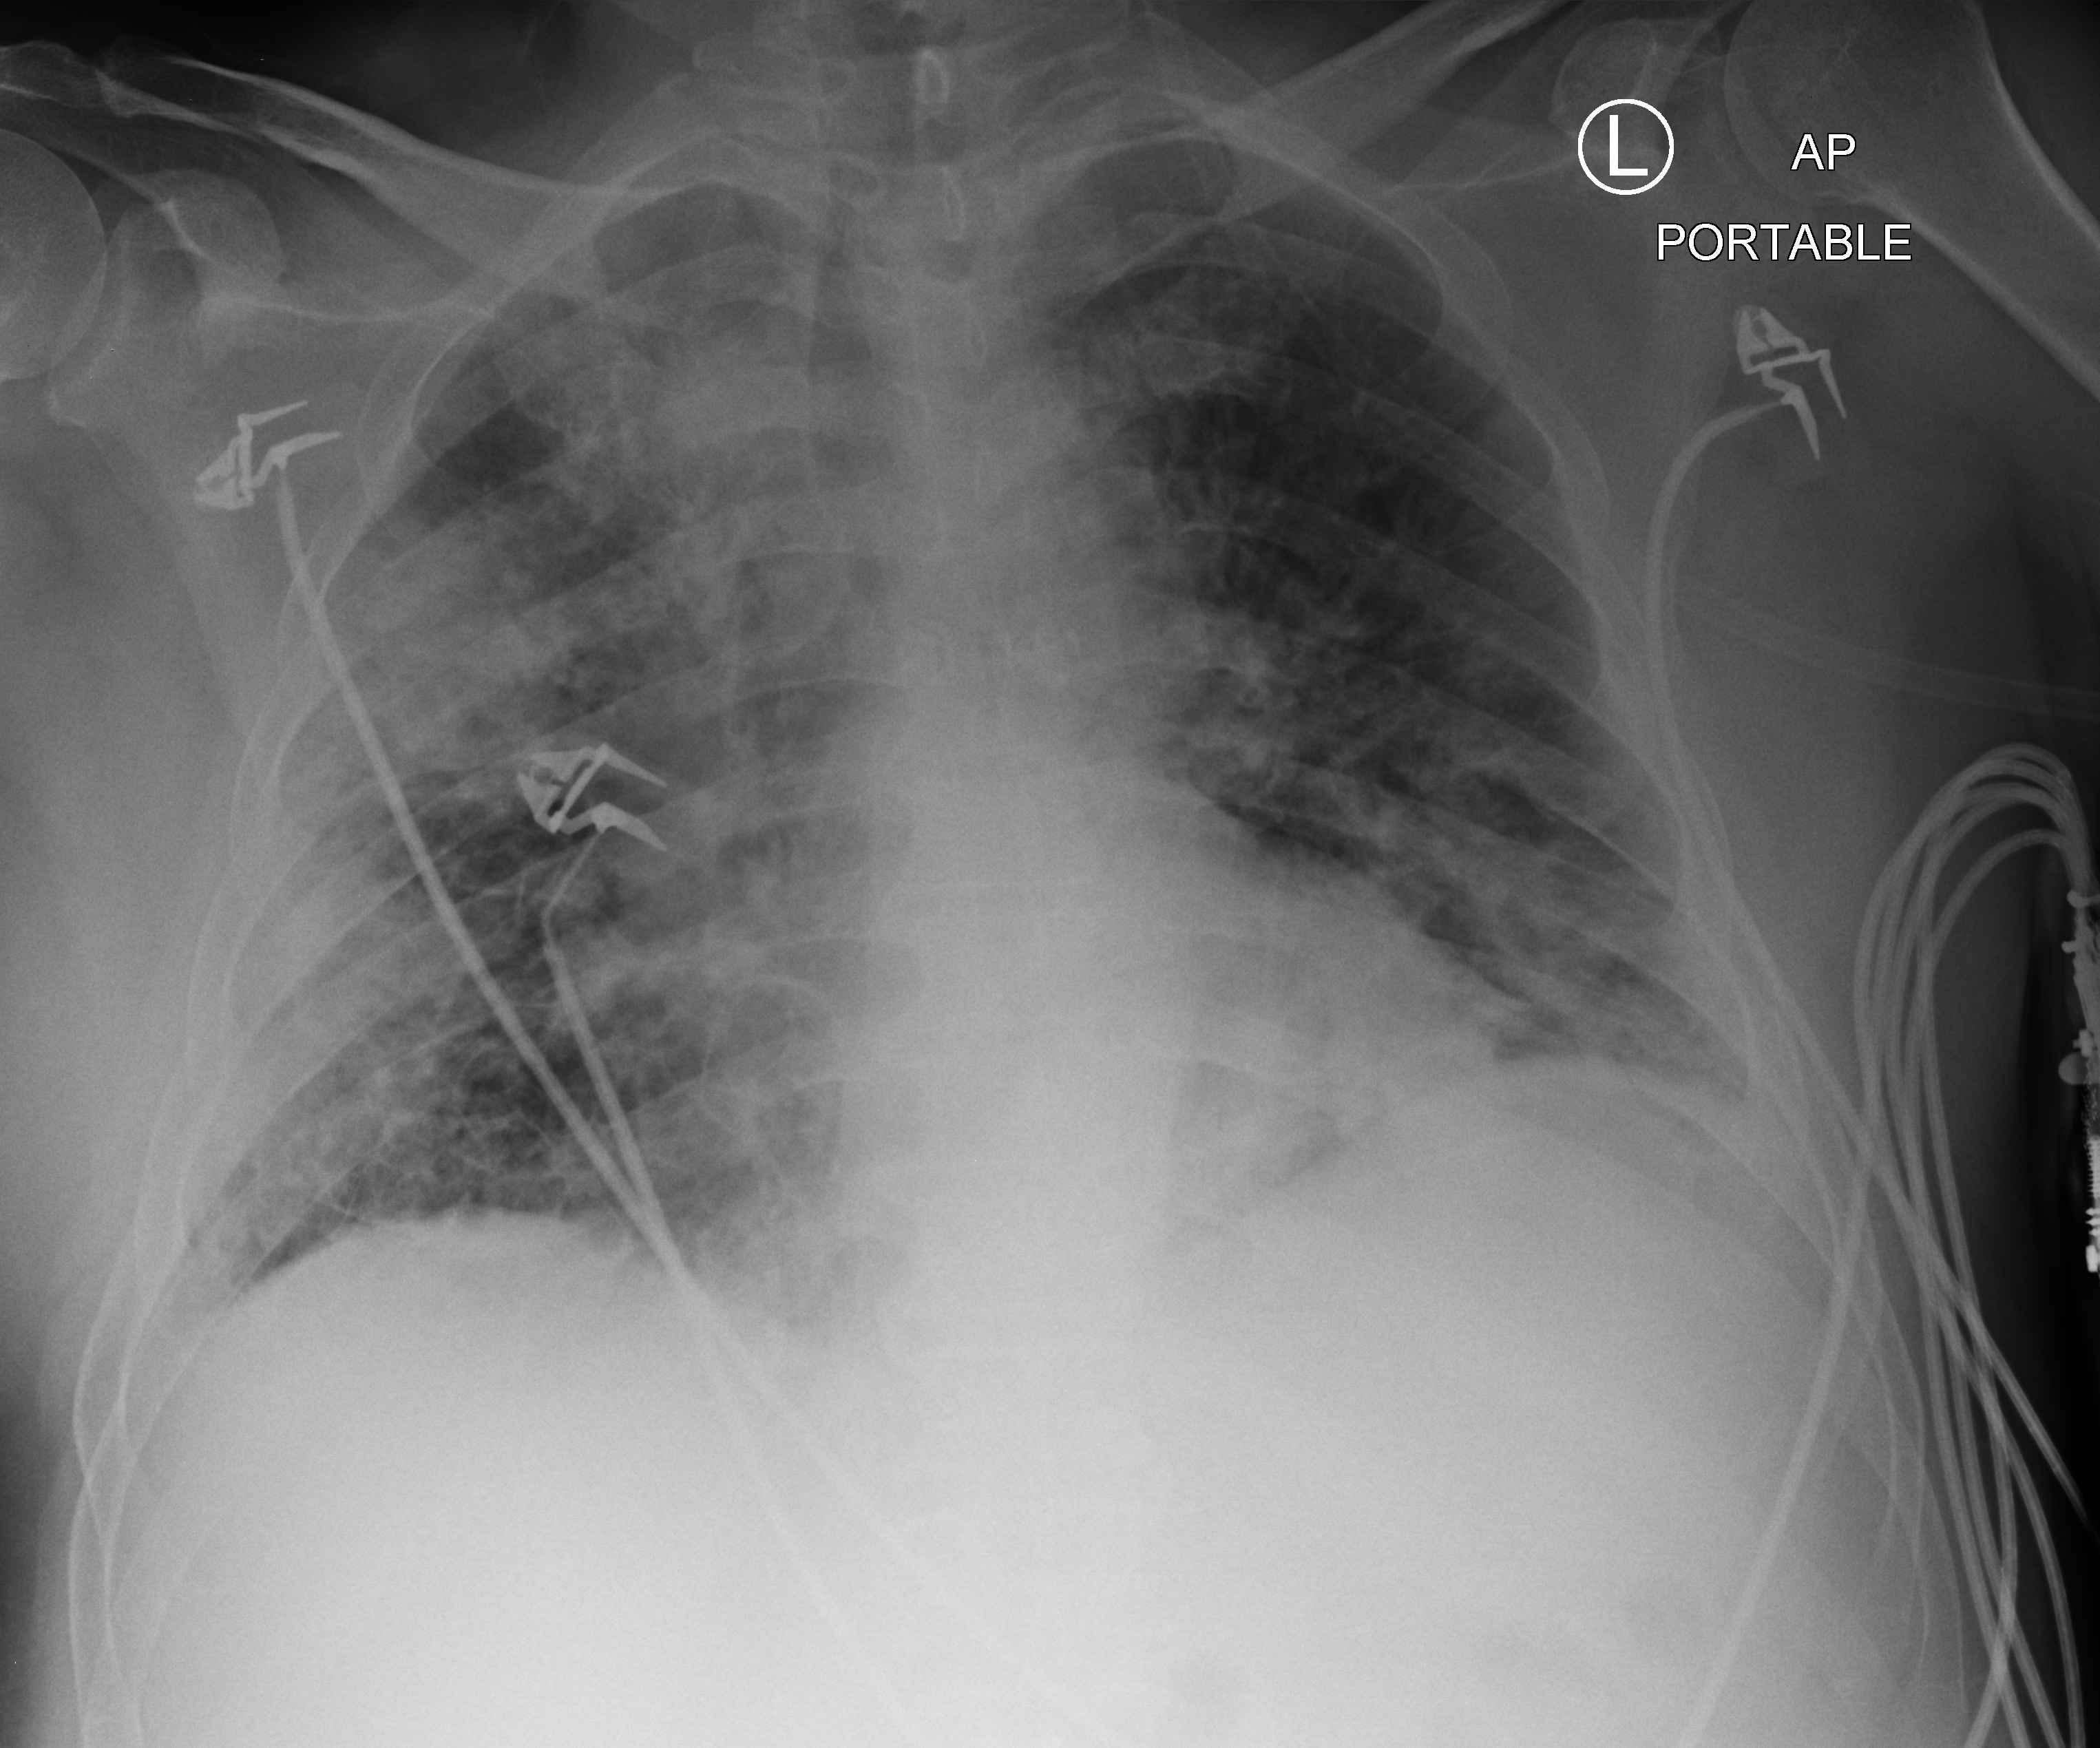
Portable chest radiograph. Male patient hospitalised with COVID-19, age 60–74 years.
Hospital-stay facts (about this admission, not read from this image; timing relative to this image not recorded): mechanically ventilated during this hospital stay: no.